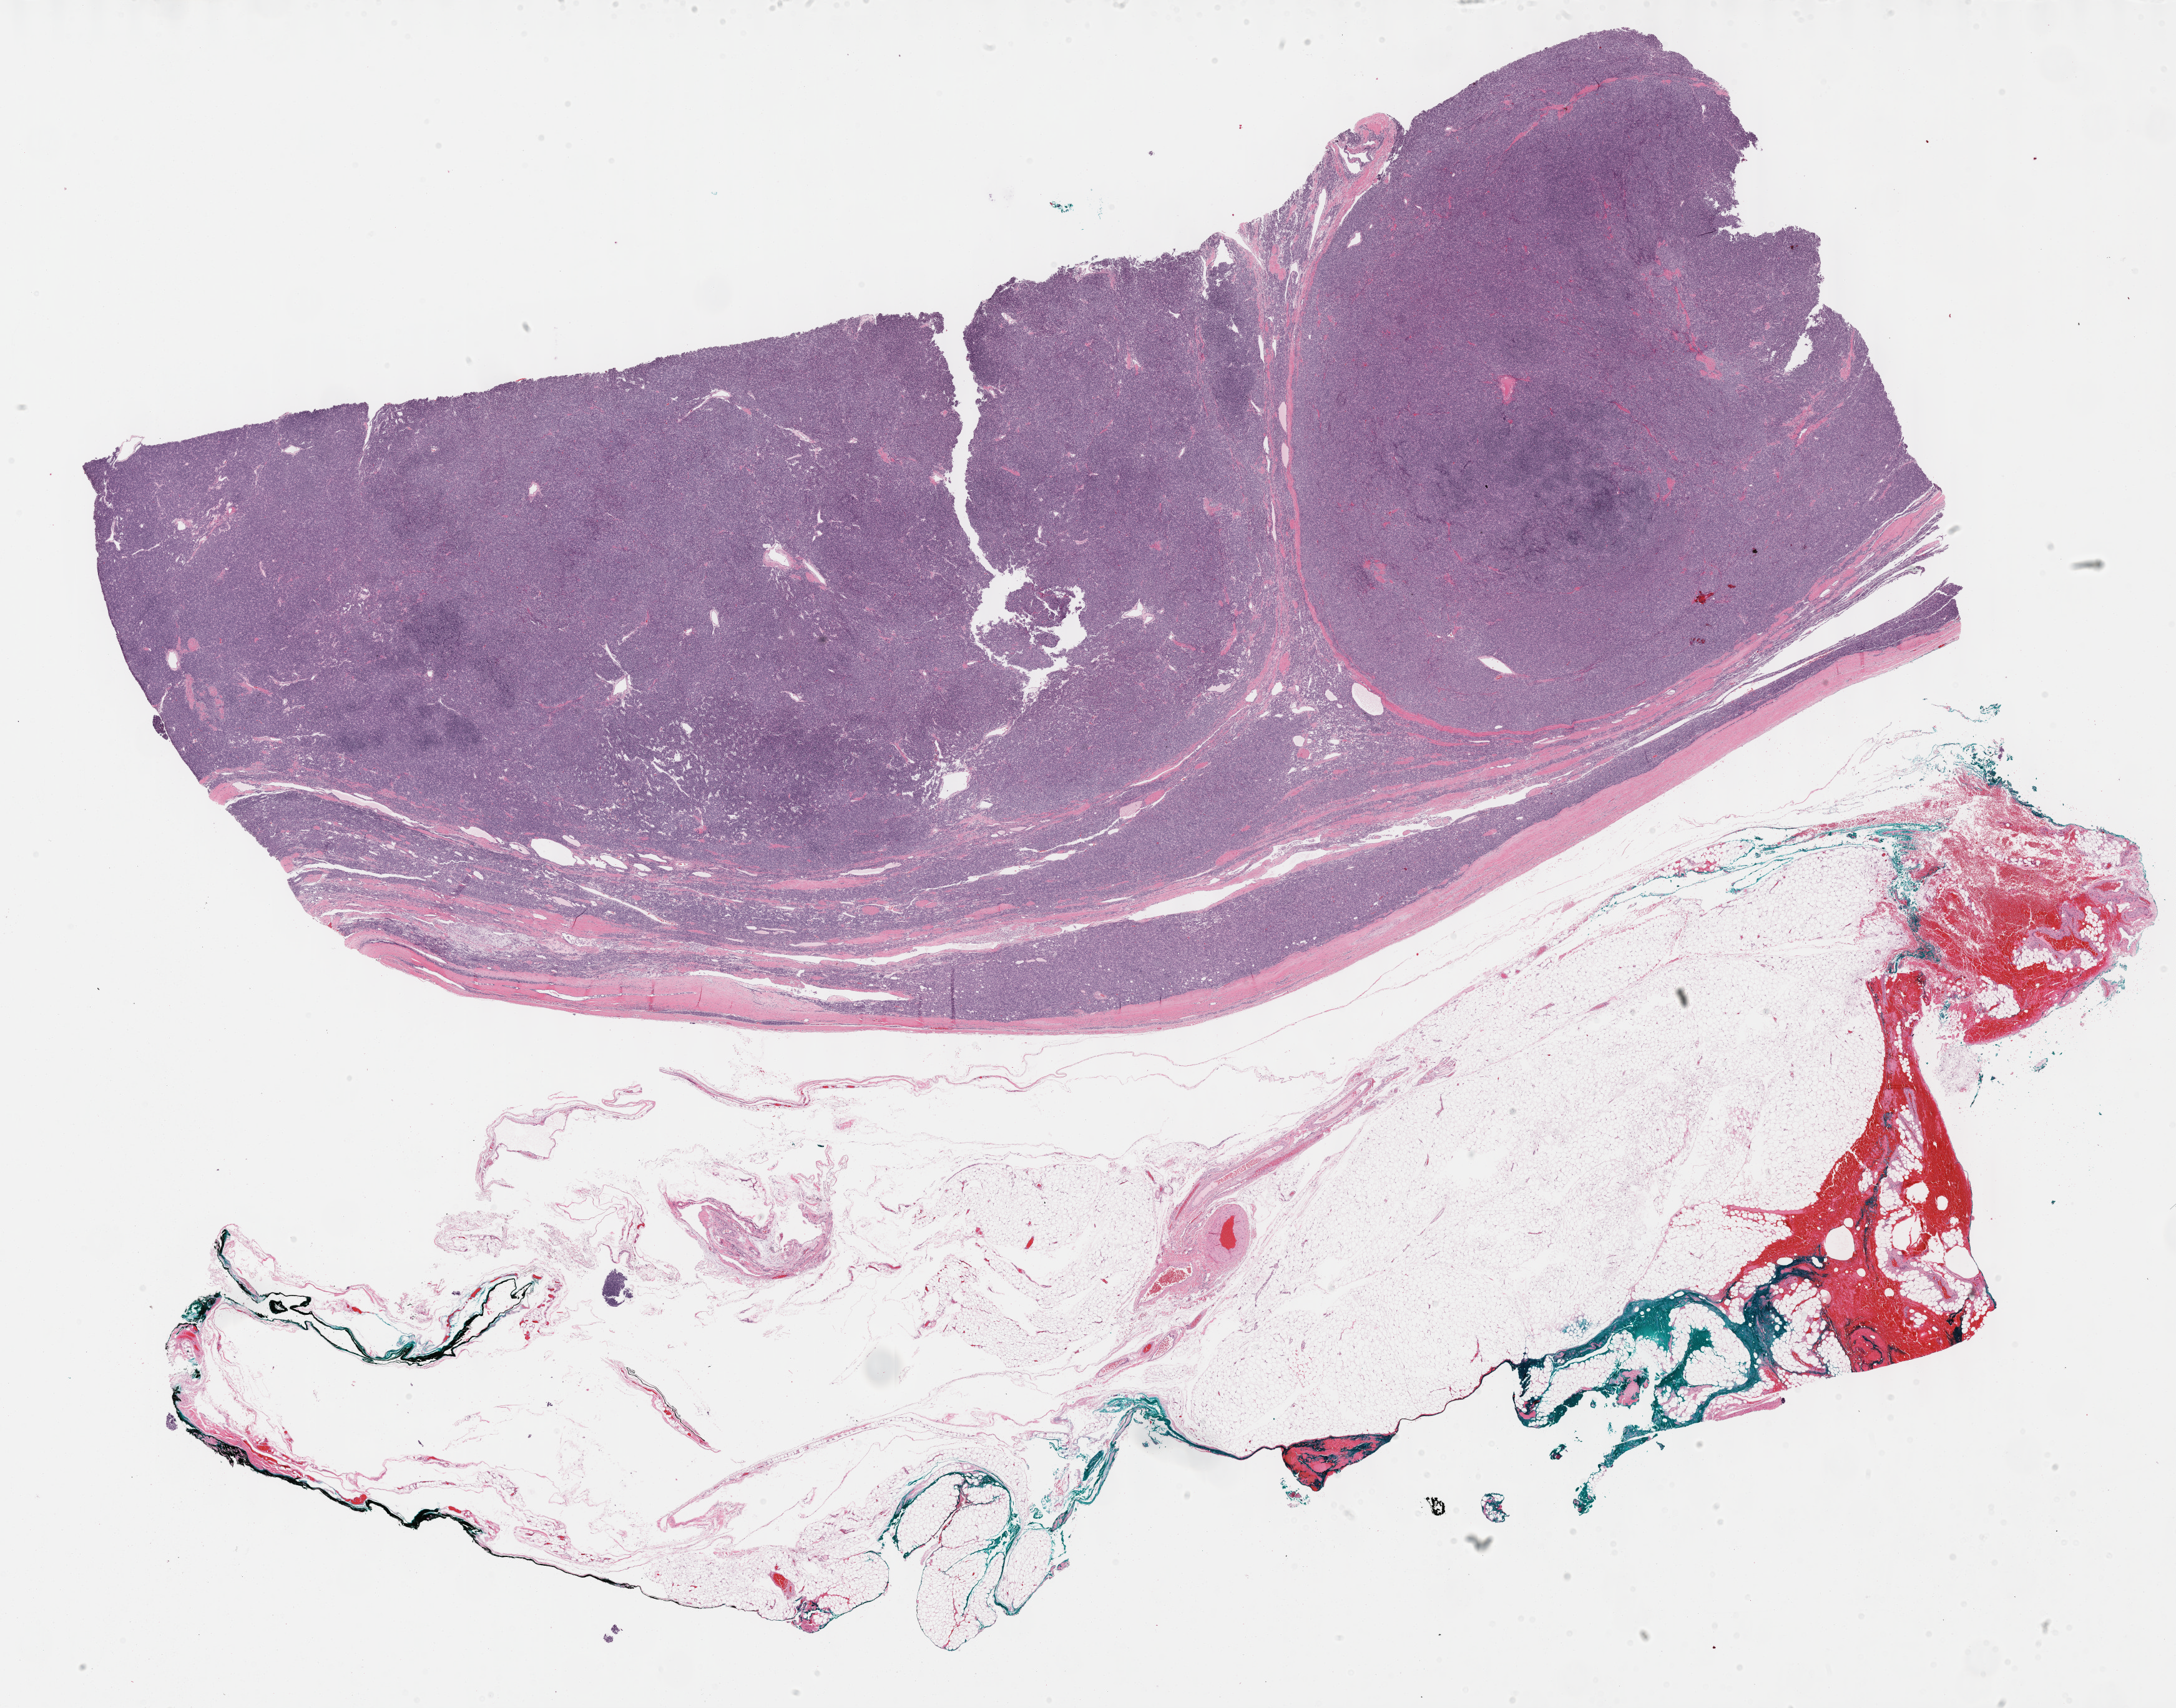
Digitized H&E-stained tissue section (whole slide) — shown as a low-resolution overview of the whole scanned area (about 28.2 x 22.1 mm, from a 40x scan). Formalin-fixed paraffin-embedded (FFPE) diagnostic section. Primary tumour sample from the thymus. Male patient; age at initial diagnosis 73 years.
* histologic diagnosis: Thymoma, type A, malignant (anterior mediastinum)